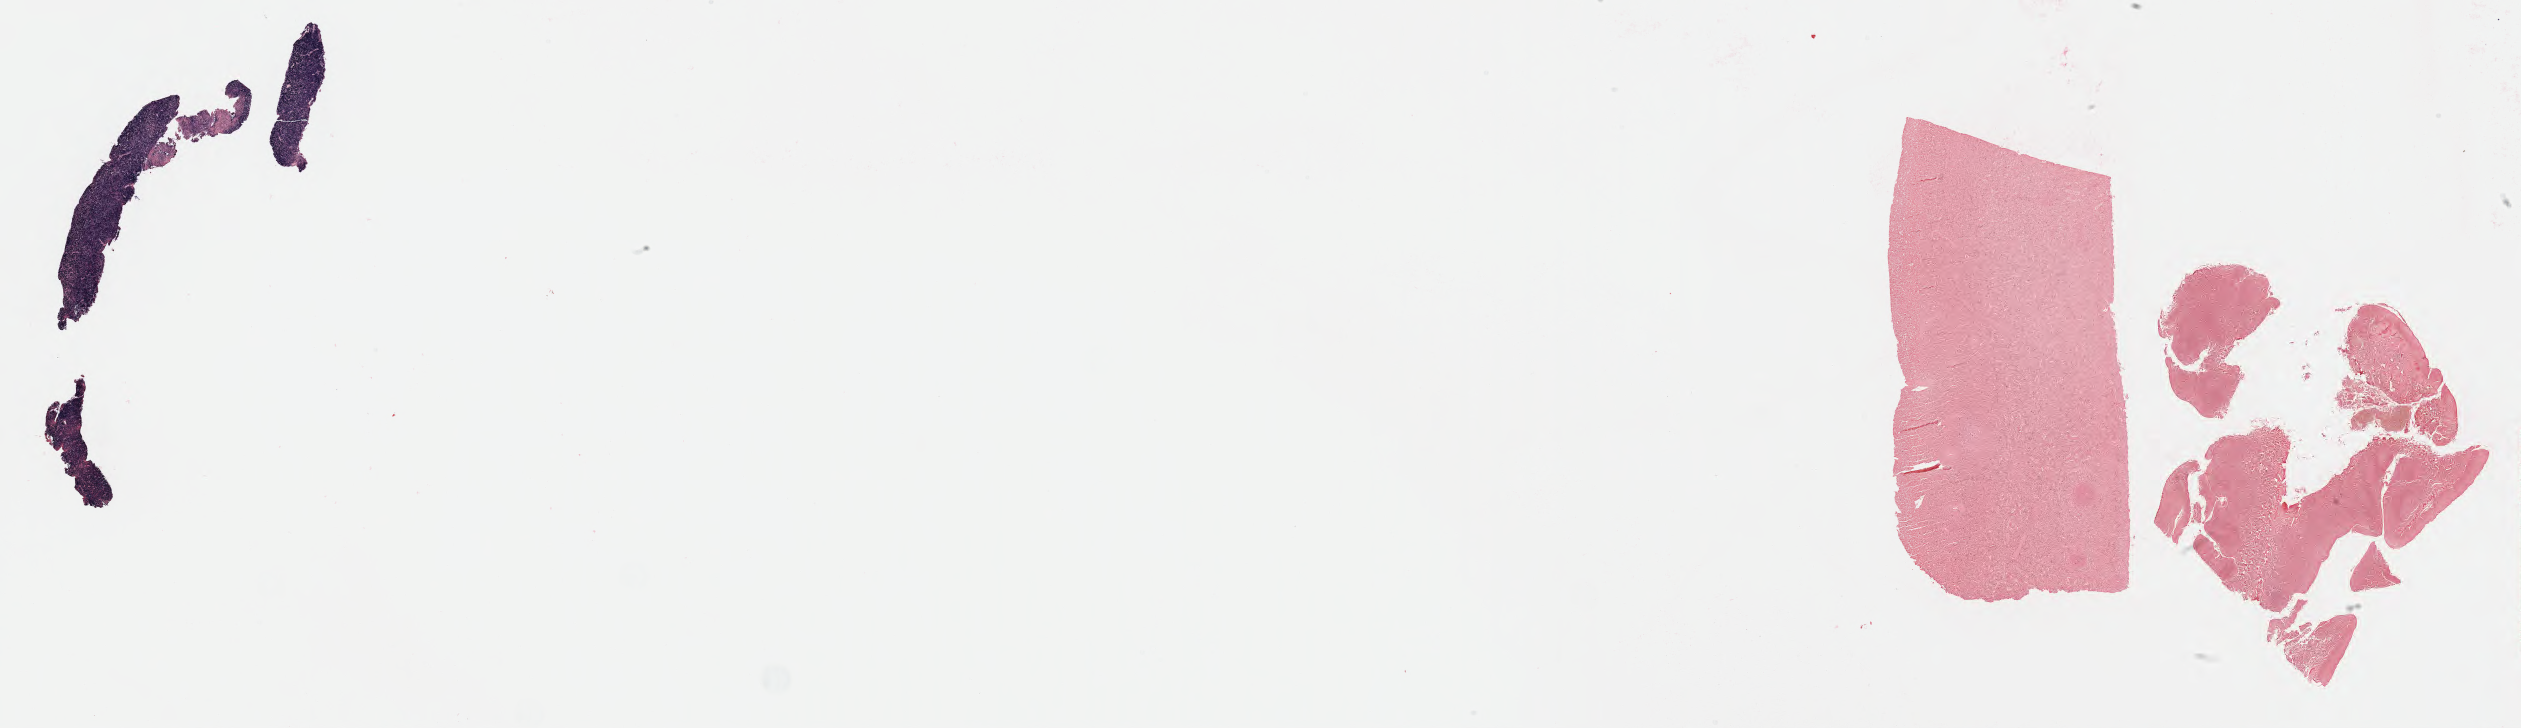
In-situ hybridisation whole-slide image, Epstein–Barr virus-encoded RNA (EBER) probe — shown as a low-resolution overview of the whole scanned area (about 40.8 x 11.8 mm); tumor tissue. Patient: male, 10 years old.
Diagnosis: Diffuse large B-cell lymphoma, NOS.